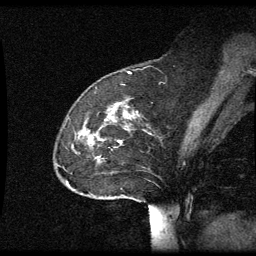
Breast MRI (dynamic contrast-enhanced), one sagittal slice; slice 19 of 60 in the series (ordered by position); dynamic contrast-enhanced series, image 2 of 3 at this slice position (ordered by acquisition); 1.5 T; TE 4.2 ms, TR 8.9 ms; 2 mm slice thickness; 256 × 256 image matrix. Patient: female, 49 years. From the clinical record (not read from this slice): setting: breast cancer imaged before/during neoadjuvant chemotherapy; receptor status: HR-positive, HER2-negative.
Annotated regions visible in this slice (semi-automatically segmented with operator editing):
- analysis volume of interest (the breast-tissue region the enhancement analysis was run in; not a lesion): bounding box <56,100,152,203> (left, top, right, bottom; pixels)
- tumour enhancement mask (voxels above the 70 % enhancement threshold inside the analysis volume of interest): <120,140,122,143>